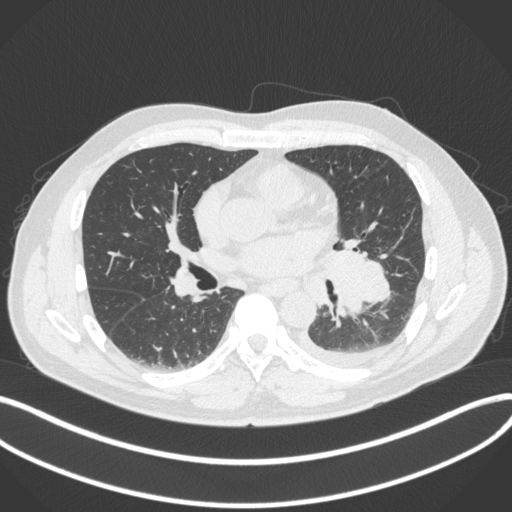
Chest CT, one axial slice. Slice 183 of 350 in the series (ordered by position). Reconstruction kernel B31f. Lung window (W 1500 / L -600 HU). 1 mm slice thickness. 512 × 512 image matrix, field of view 400 × 400 mm. Patient: male, 58 years. Case-level facts recorded for this patient, not image findings: clinical TNM (as recorded): T3 N1 M1b.
Structures marked on this image (bounding box drawn by a radiologist):
- lung tumour (recorded histology: small cell carcinoma): bounding box [x1, y1, x2, y2] px = [319, 239, 398, 325]